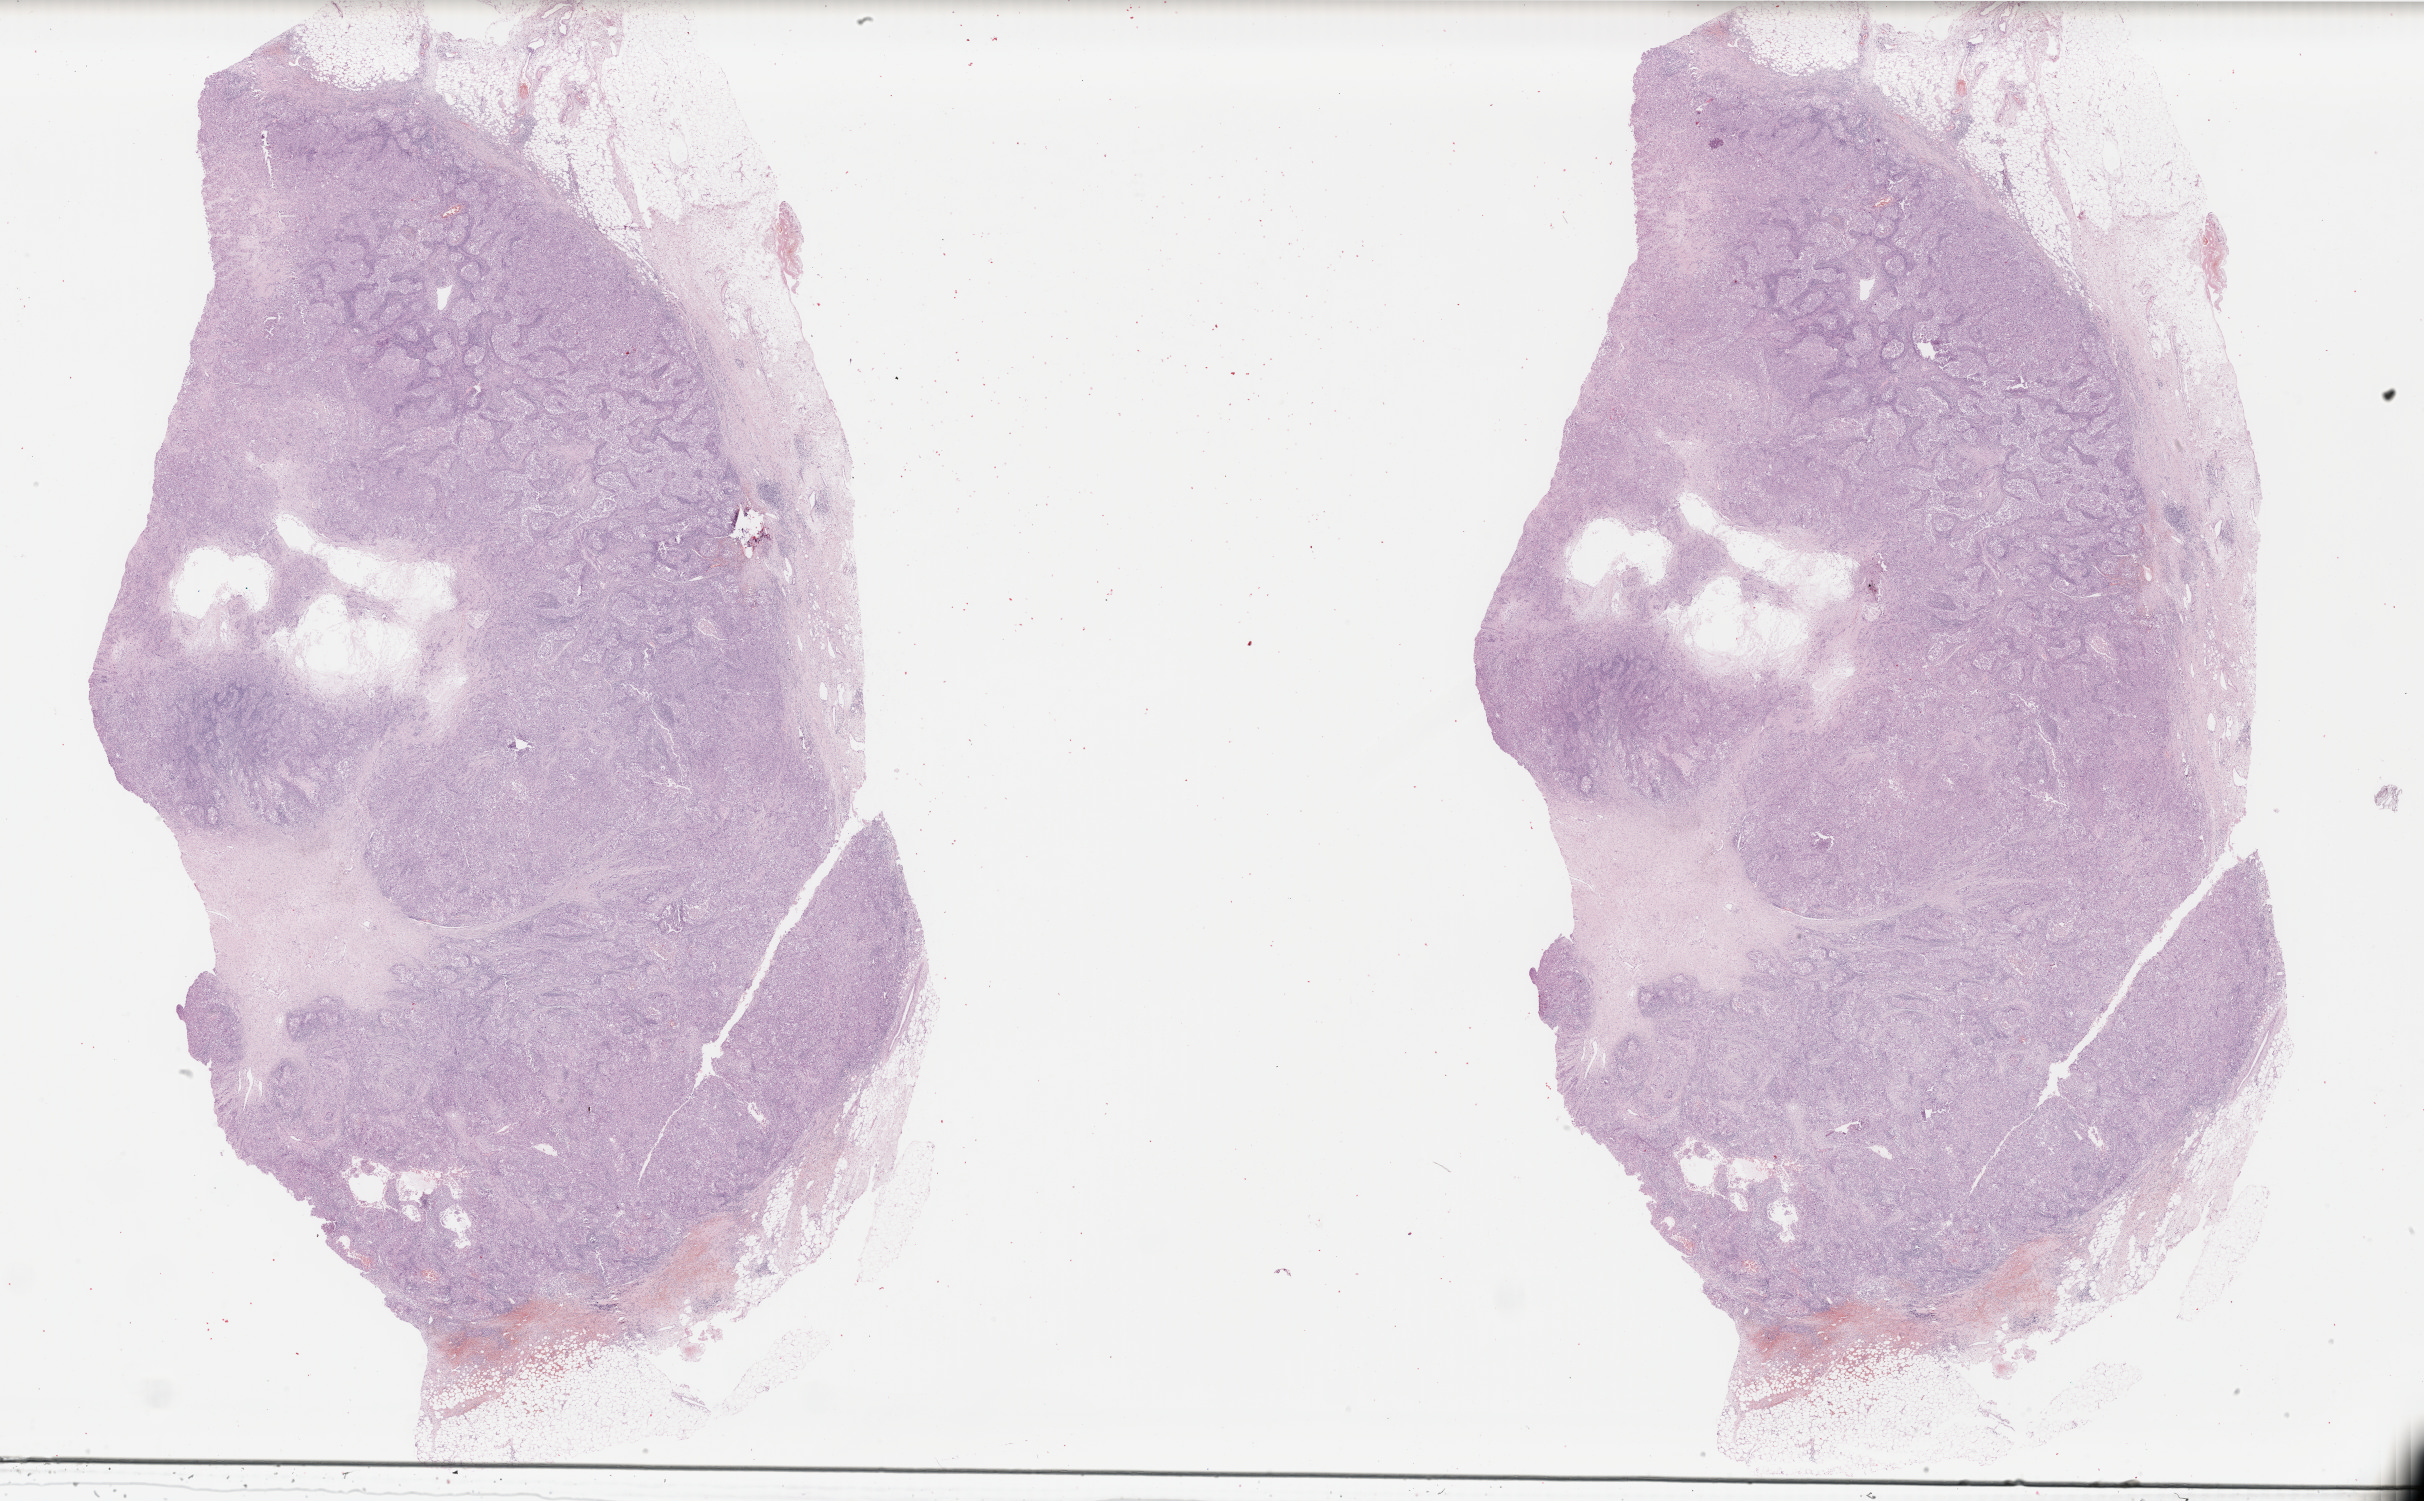
H&E whole-slide image, low-resolution overview of the scanned area, about 38.5 x 23.8 mm (acquisition: 40x scan). FFPE section. Primary tumour sample from the breast. Female, age 72 years at initial diagnosis.
AJCC pathologic stage: IIA (7th edition). Diagnosis: Infiltrating duct carcinoma, NOS.